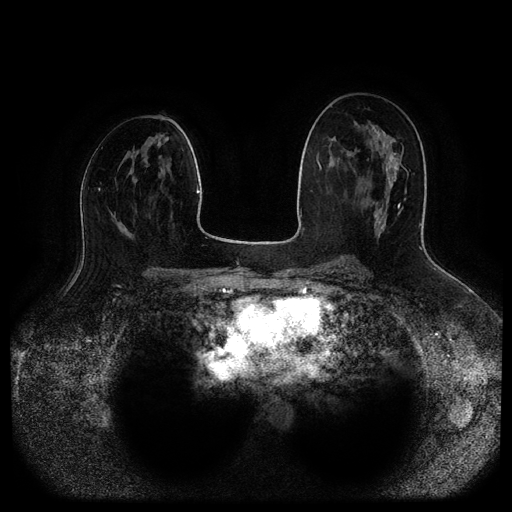
Breast MRI (dynamic contrast-enhanced, multi-phase), one axial slice; slice 51 of 116 in the series (ordered by position); dynamic contrast-enhanced series, time point 2 of 5 at this slice position (early post-contrast); 1.5 T; TE 2.6 ms, TR 5.2 ms; 2 mm slice thickness; 512 × 512 image matrix, field of view 380 × 380 mm. Patient: female, 45 years.
Structures marked on this image (semi-automatic segmentation, software-assisted and operator-edited):
- breast lesion (labelled benign in the annotation): bounding box <367,144,399,168> (left, top, right, bottom; pixels)